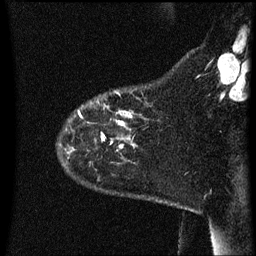
Breast MRI (dynamic contrast-enhanced), one sagittal slice. Dynamic contrast-enhanced series, image 2 of 3 at this slice position (ordered by acquisition). 1.5 T. TE 4.2 ms, TR 8.4 ms. 2.2 mm slice thickness. 256 × 256 image matrix, field of view 200 × 200 mm. Female patient, age 35 years. From the clinical record (not read from this slice): setting: breast cancer imaged before/during neoadjuvant chemotherapy; receptor status: HER2-positive.
Outlined on this slice (semi-automatically segmented with operator editing):
- analysis volume of interest (the breast-tissue region the enhancement analysis was run in; not a lesion): bounding box (x1, y1, x2, y2) in pixels: (61, 92, 142, 163)
- tumour enhancement mask (voxels above the 70 % enhancement threshold inside the analysis volume of interest): (119, 116, 132, 127)